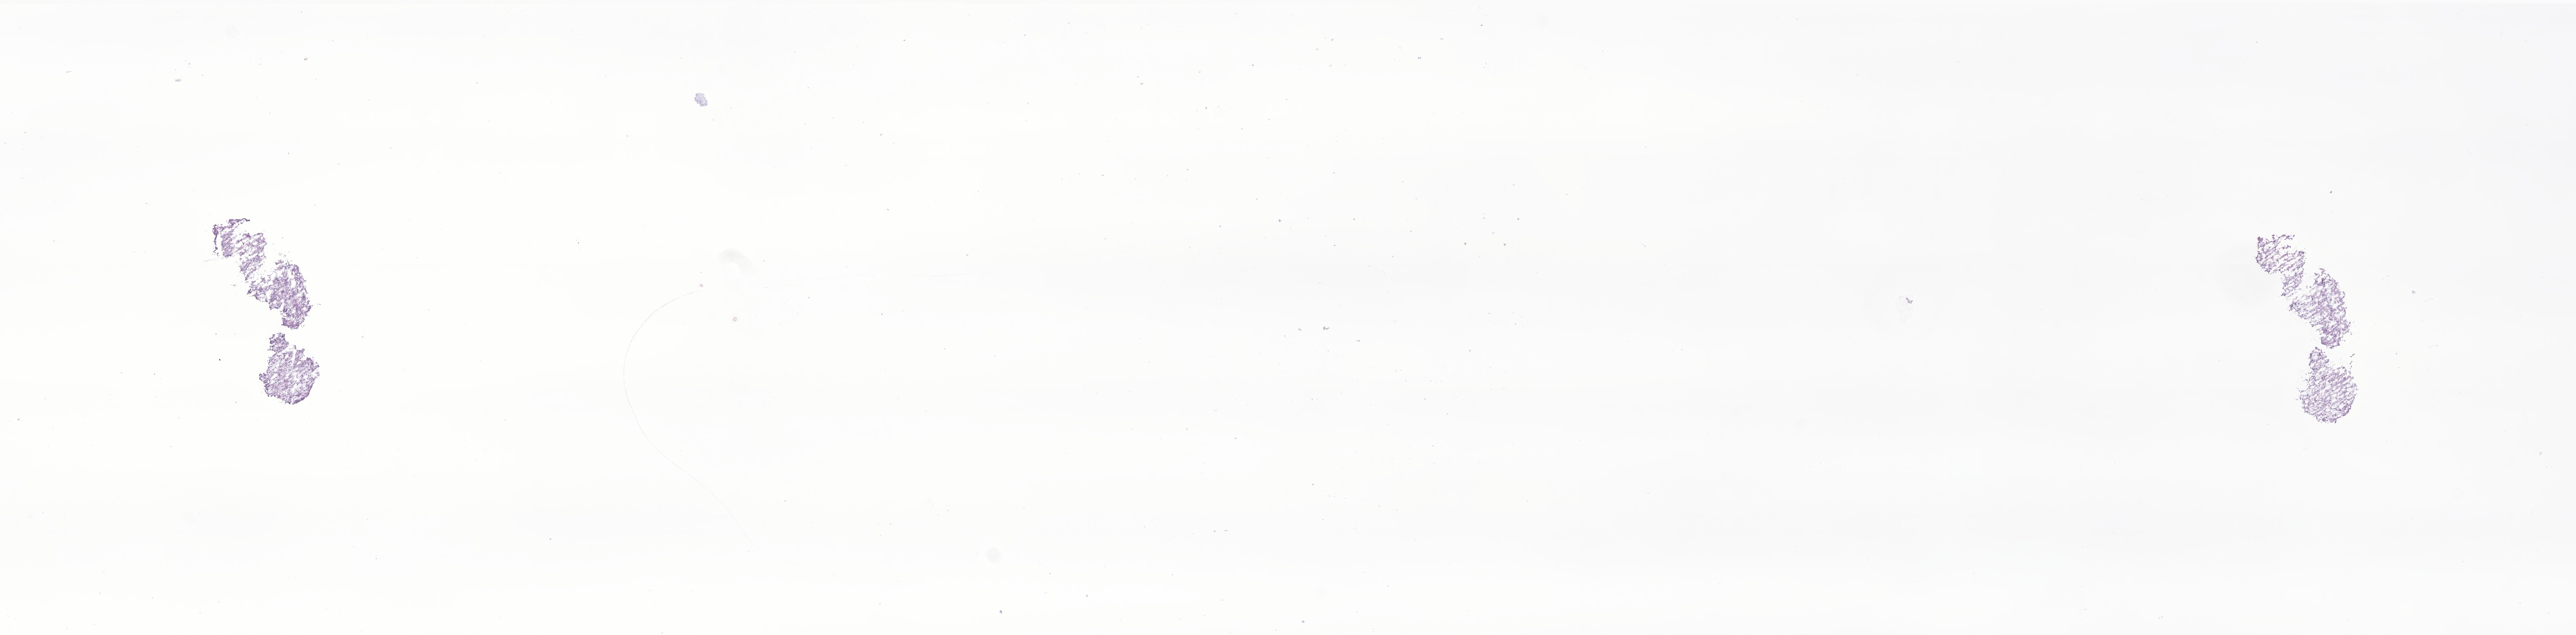
Whole-slide image, H&E stain of tumor tissue from the brain — low-resolution overview of the scanned area, about 22.1 x 5.4 mm. Frozen section (OCT-embedded). Patient: male, age 290 days.
* diagnosis (ICD-O-3 morphology term): Pilocytic astrocytoma